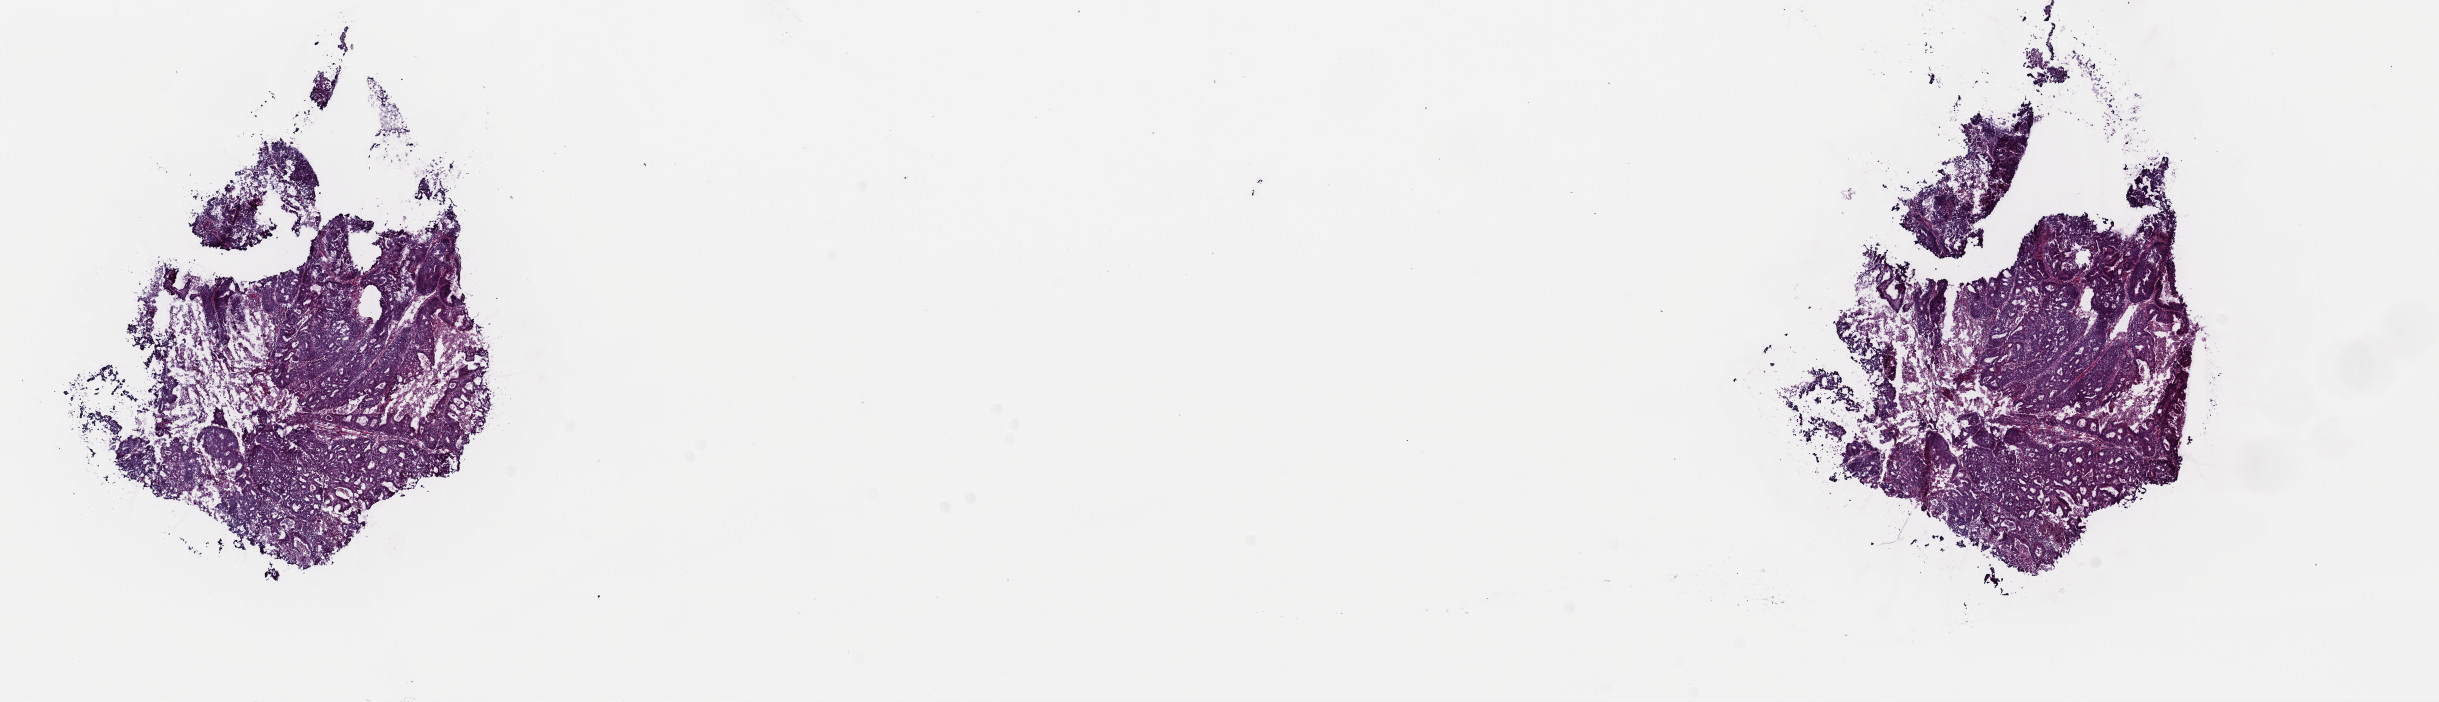
Digitized H&E-stained tissue section (whole slide), low-resolution overview of the scanned area, about 19.3 x 5.5 mm (from a 40x scan), frozen section from the top of the tissue portion, uterus, primary tumour sample. Female, age 73 years at initial diagnosis. Histologic grade: G3 (poorly differentiated). Composition of this section per pathologist review: tumour cells 85%, tumour nuclei 80%, normal cells 0%, stromal cells 0%, necrosis 15%. Inflammatory infiltration, as recorded: lymphocyte infiltration 1%, monocyte infiltration 5%, neutrophil infiltration 5%.
- pathologic diagnosis: Endometrioid adenocarcinoma, NOS (endometrium)
- FIGO stage: IB